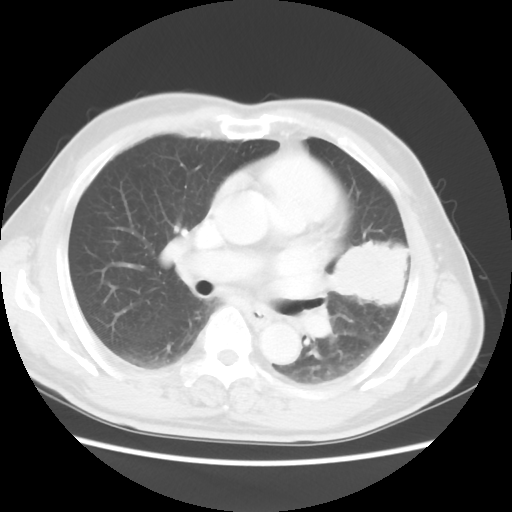
Chest CT, one axial slice; slice 28 of 50 in the series (ordered by position); lung window (W 1500 / L -600 HU); 5 mm slice thickness; 512 × 512 image matrix, field of view 360 × 360 mm. Male patient, age 69 years. Case-level facts recorded for this patient, not image findings: clinical TNM (as recorded): T3 N1 M1a.
Annotated regions visible in this slice (rectangle marked by the reading radiologist):
- lung tumour (recorded histology: squamous cell carcinoma): bounding box <322,233,431,333> (left, top, right, bottom; pixels)